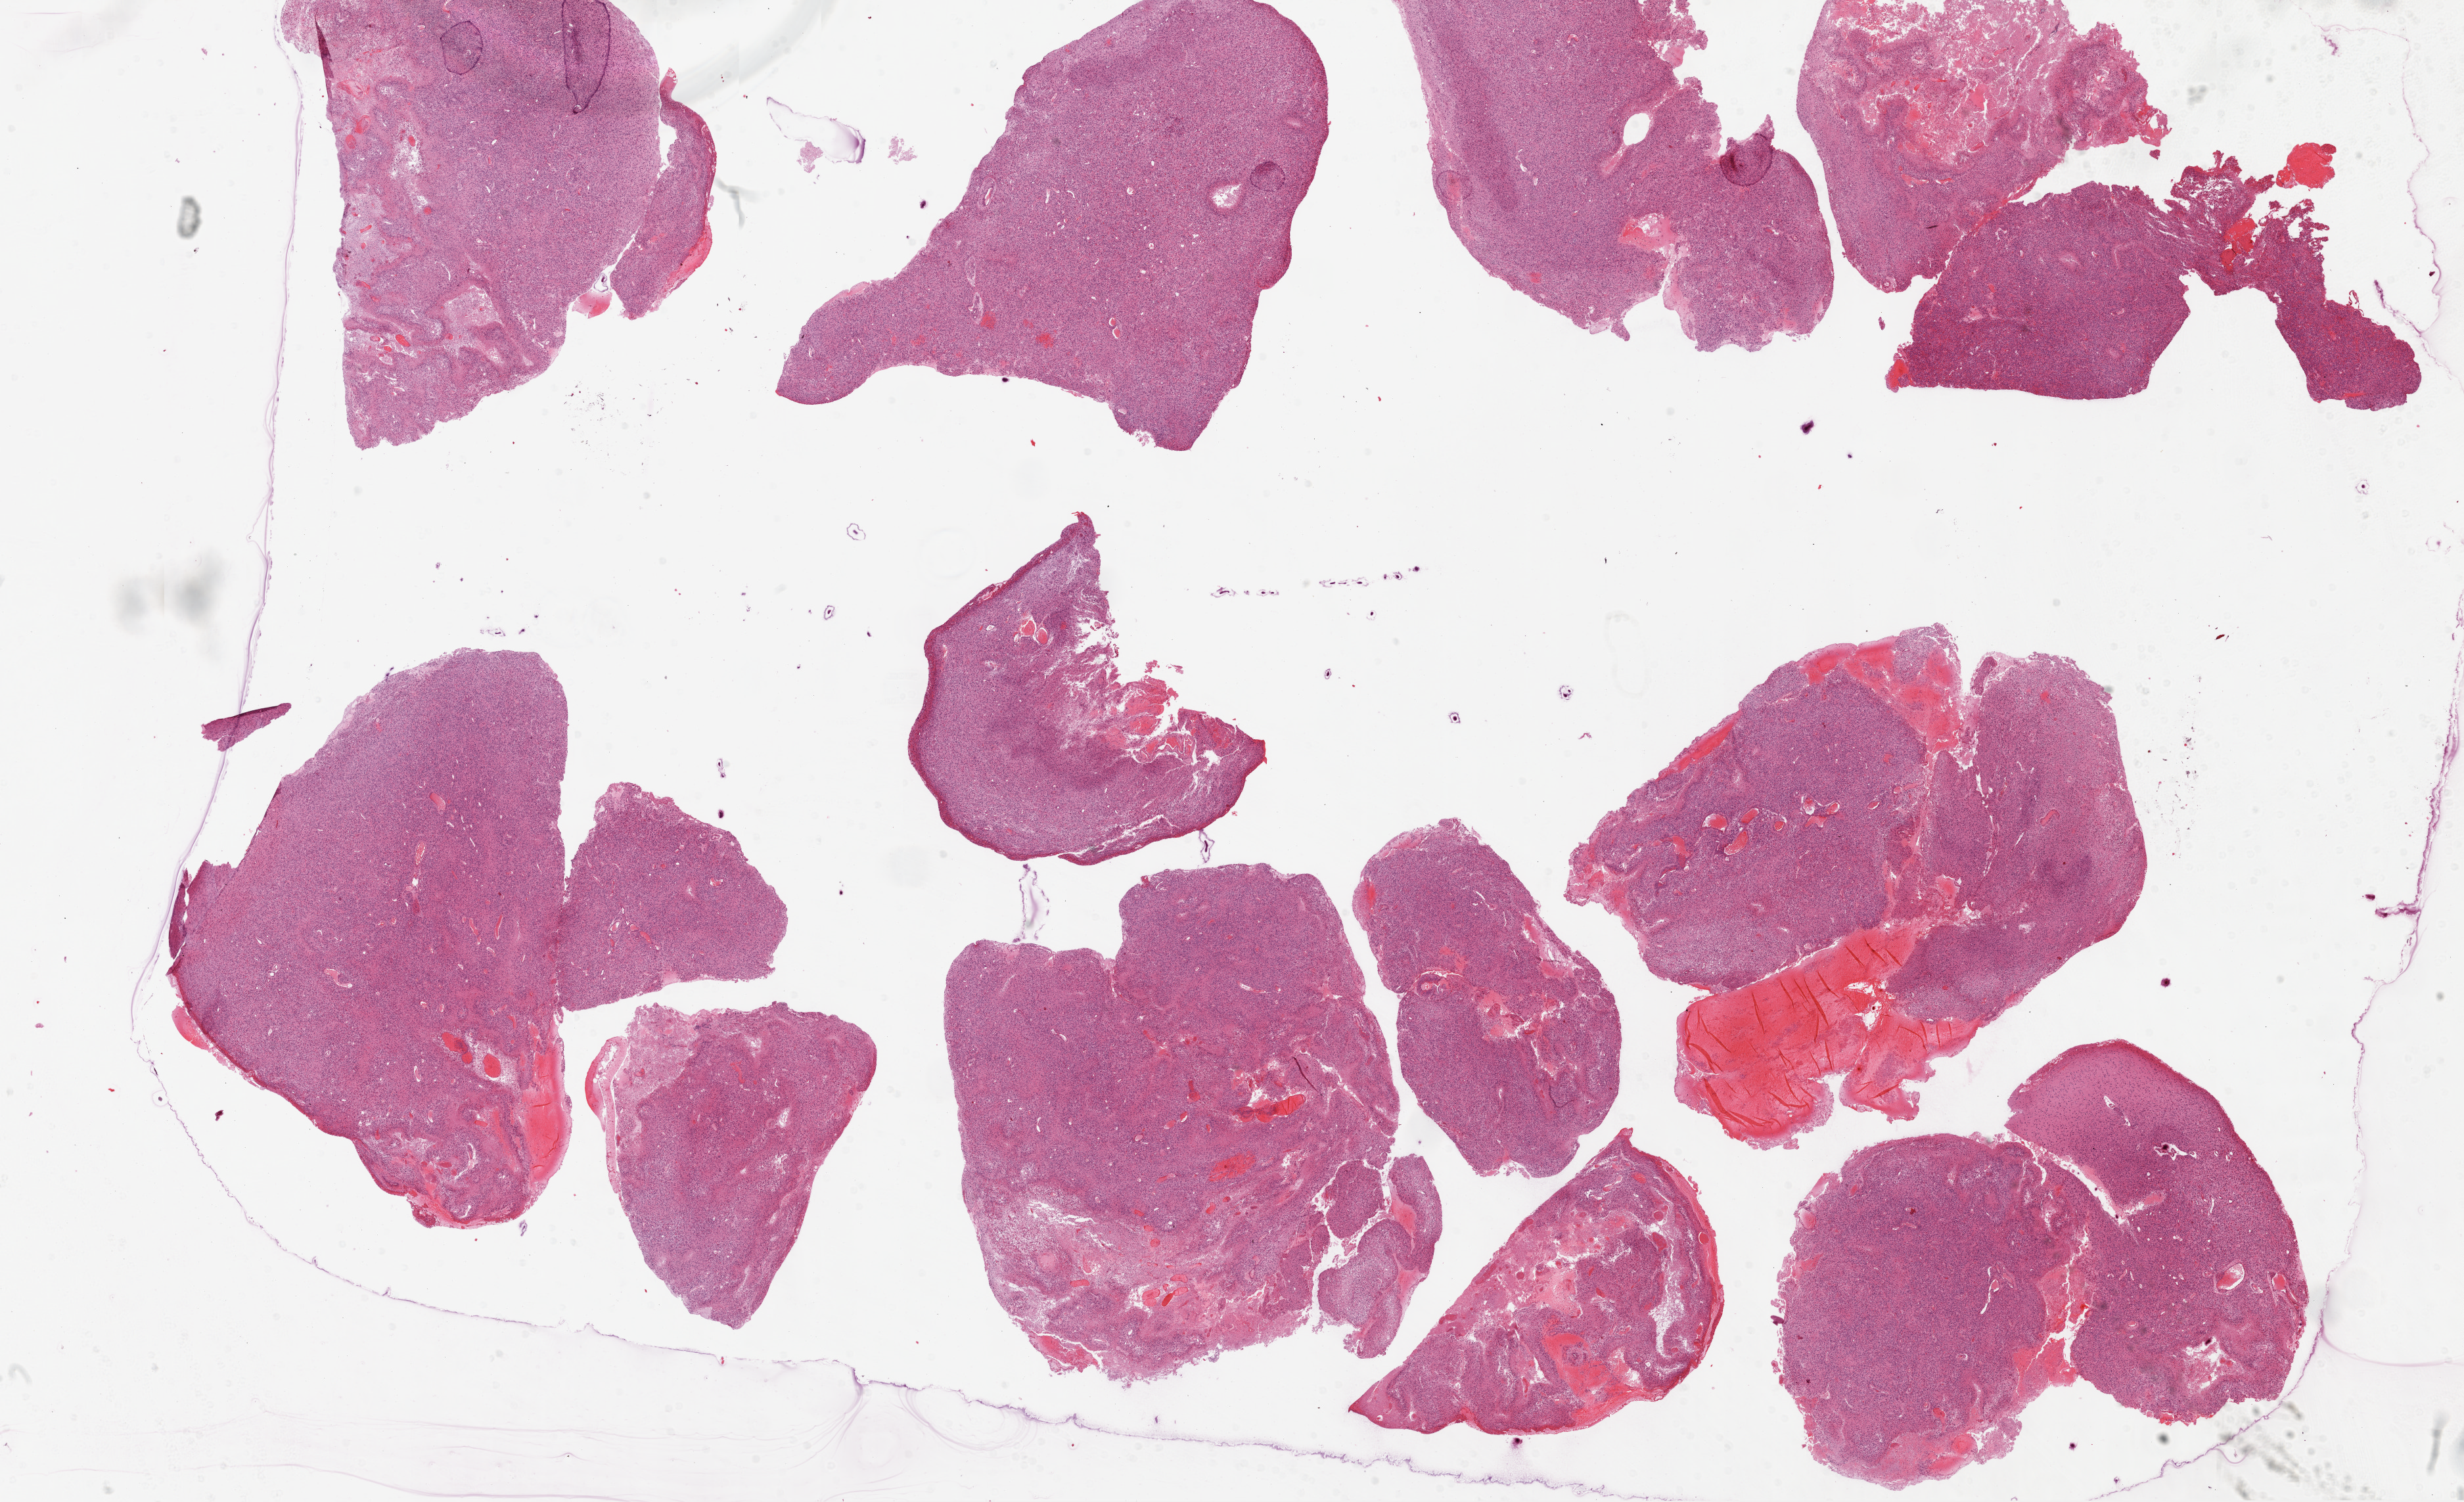
Digitized H&E-stained tissue section (whole slide), whole scanned area (about 30.1 x 18.3 mm) shown as a low-resolution overview, formalin-fixed paraffin-embedded (FFPE) diagnostic section, sample: primary tumour, brain. Patient: male, age at initial diagnosis 36 years.
Histologic diagnosis: Glioblastoma.